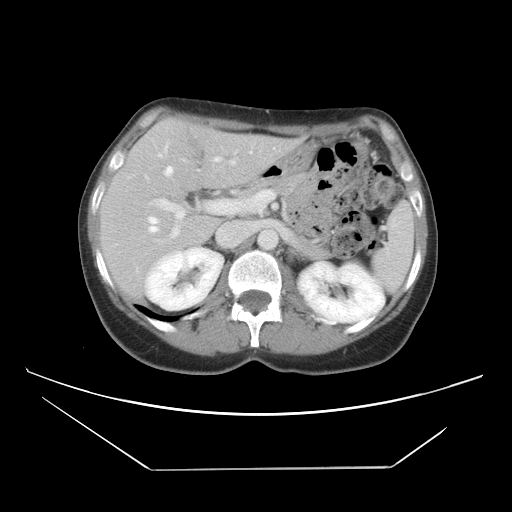
Contrast-enhanced abdominal CT, one axial slice. Slice 26 of 42 in the series (ordered by position). Intravenous contrast given. Soft-tissue window (W 400 / L 40 HU). 5 mm slice thickness. 512 × 512 image matrix, field of view 399 × 399 mm. Female patient, age 52 years. From the clinical record (not read from this slice): diagnosis: colorectal cancer liver metastases, imaged before liver resection.
Outlined on this slice (expert manual segmentation):
- hepatic veins: bounding box <147,140,253,234> (left, top, right, bottom; pixels)
- liver: <102,120,293,296>
- planned liver remnant (the part of the liver to remain after resection): <114,121,219,198>
- portal vein (with intrahepatic branches): <149,149,276,238>